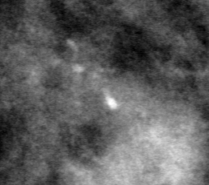
Region of interest cut from a scanned film mammogram (one marked finding), right breast, MLO view.
Finding: calcifications, morphology pleomorphic, distribution clustered; BI-RADS assessment category 4; subtlety rating 2 on a 1 (subtle) to 5 (obvious) scale; pathology (as recorded): malignant.